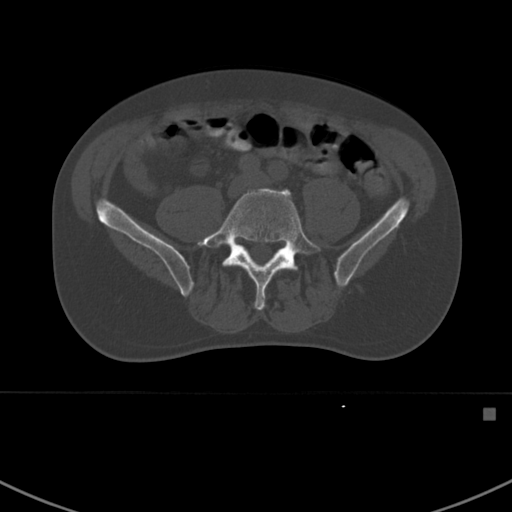
CT including the spine, one axial slice. Slice 220 of 412 in the series (ordered by position). 120 kVp. Bone window (W 1800 / L 400 HU). 1.5 mm slice thickness. 512 × 512 image matrix, field of view 358 × 358 mm. Male patient, age 59 years. Case-level facts recorded for this patient, not image findings: primary cancer: prostate.
Structures marked on this image (semi-automatic segmentation, software-assisted and operator-edited):
- L5 vertebra: box from (x=198, y=188) to (x=320, y=311) px